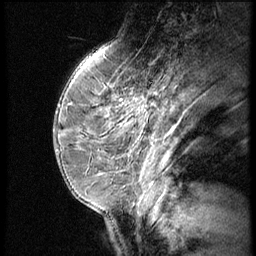
Breast MRI (dynamic contrast-enhanced), one sagittal slice. Position 21 of 62 along the scan axis. 3 images stored at this slice position (order not interpretable as contrast timing). 1.5 T. TE 4.2 ms, TR 9 ms. 2.5 mm slice thickness. 256 × 256 image matrix, field of view 180 × 180 mm. Female patient, age 39 years. From the clinical record (not read from this slice): setting: breast cancer imaged before/during neoadjuvant chemotherapy; receptor status: triple-negative.
Annotated regions visible in this slice (semi-automatically segmented with operator editing):
- analysis volume of interest (the breast-tissue region the enhancement analysis was run in; not a lesion): bounding box (x1, y1, x2, y2) in pixels: (94, 70, 173, 156)
- tumour enhancement mask (voxels above the 140 % enhancement threshold inside the analysis volume of interest): (152, 103, 154, 105)